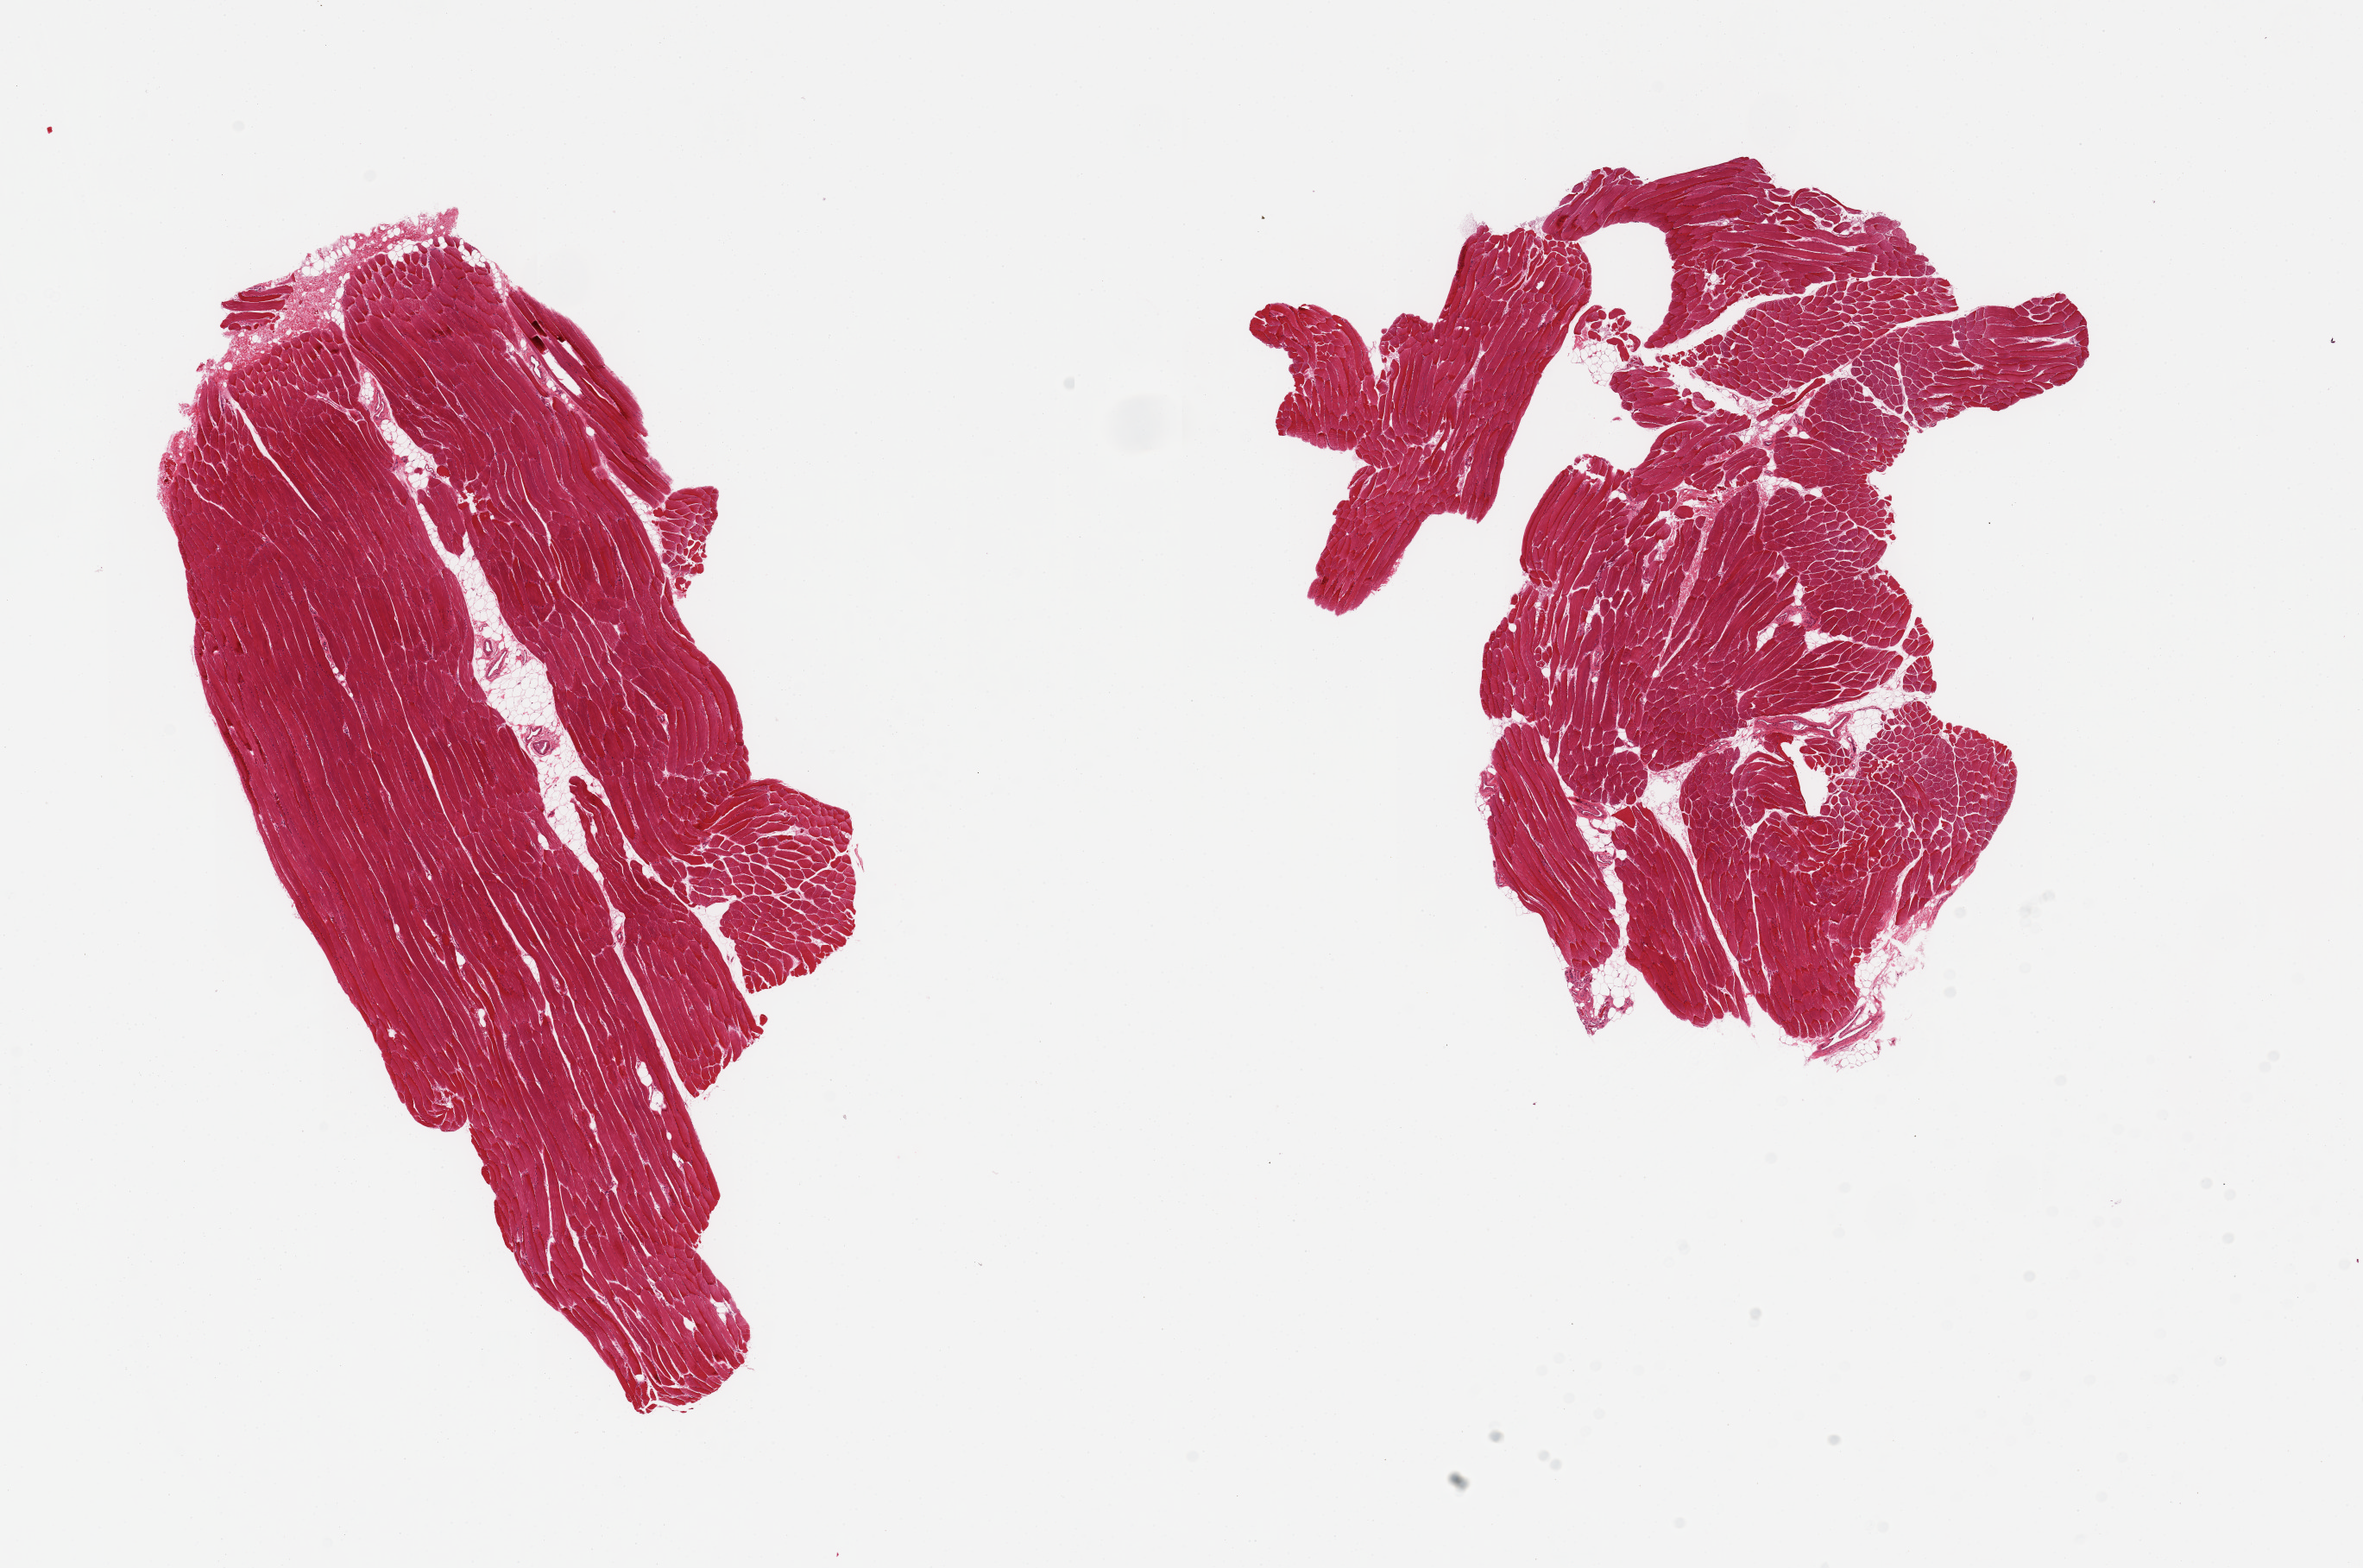
Digitized hematoxylin and eosin (H&E)-stained section, brightfield — a low-resolution overview of the entire scanned area, about 21.7 x 14.4 mm (from a 20x scan). PAXgene-fixed paraffin-embedded (PFPE) section. Target tissue: skeletal muscle. Donor tissue sample. Donor: male.
* review note (as recorded): 2 pieces; <10% internal fat